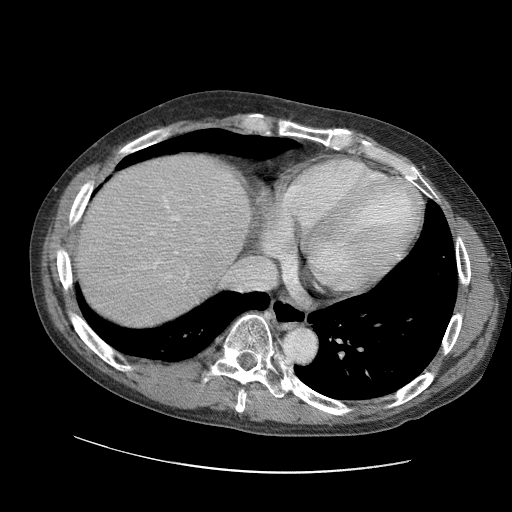
Contrast-enhanced abdominal CT (liver protocol), one axial slice. Reconstruction kernel STANDARD. Soft-tissue window (W 400 / L 40 HU). 2.5 mm slice thickness. 512 × 512 image matrix, field of view 400 × 400 mm. From the clinical record (not read from this slice): diagnosis: hepatocellular carcinoma (patient treated with transarterial chemoembolisation; whether this scan precedes or follows treatment is not stated here); TNM stage (as recorded): Stage-IIIC; Child-Pugh class: B; tumour nodularity: uninodular.
Outlined on this slice (semi-automatically segmented with operator editing):
- liver parenchyma outside the tumour (the mass and vessels are separate outlines, so this box may not span the whole liver): bounding box [x1, y1, x2, y2] px = [68, 152, 250, 326]
- liver vessels: [142, 190, 224, 291]